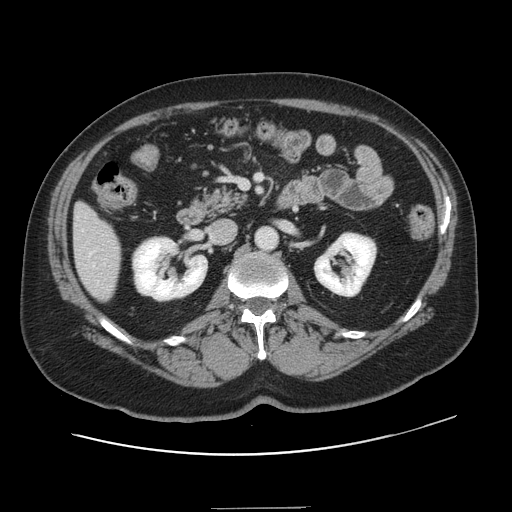
Contrast-enhanced abdominal CT, one axial slice; position 57 of 143 along the scan axis; 120 kVp; intravenous contrast given; soft-tissue window (W 400 / L 40 HU); 2.5 mm slice thickness; 512 × 512 image matrix. Male patient, age 62 years. Case-level facts recorded for this patient, not image findings: diagnosis: colorectal cancer liver metastases, imaged before liver resection; multiple liver metastases: yes; largest metastasis: 2.7 cm; chemotherapy before resection: yes.
Structures marked on this image (outlined manually by an expert reader):
- hepatic veins: bounding box (x1, y1, x2, y2) in pixels: (89, 253, 95, 267)
- liver: (74, 205, 121, 301)